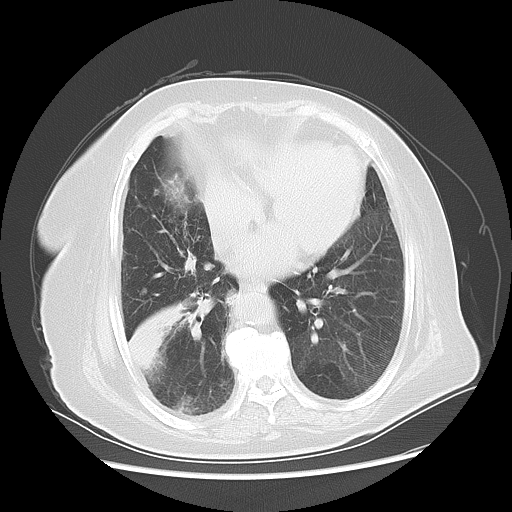
Chest CT, one axial slice; slice 22 of 56 in the series (ordered by position); reconstruction kernel LUNG; 120 kVp; lung window (W 1500 / L -600 HU); 512 × 512 image matrix, field of view 378 × 378 mm. Female patient, age 73 years. From the clinical record (not read from this slice): clinical TNM (as recorded): T3 N0 M0.
Annotated regions visible in this slice (rectangle marked by the reading radiologist):
- lung tumour (recorded histology: adenocarcinoma): bounding box <121,295,188,380> (left, top, right, bottom; pixels)